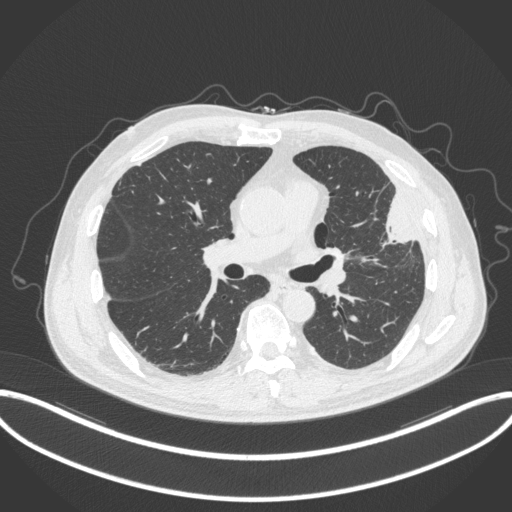
Chest CT, one axial slice. Slice 186 of 382 in the series (ordered by position). Reconstruction kernel B31f. Lung window (W 1500 / L -600 HU). 1 mm slice thickness. 512 × 512 image matrix, field of view 415 × 415 mm. Male patient, age 64 years. Case-level facts recorded for this patient, not image findings: clinical TNM (as recorded): T4 N1 M0; histopathological grade: G3.
Outlined on this slice (rectangle marked by the reading radiologist):
- lung tumour (recorded histology: adenocarcinoma): bounding box <369,186,419,248> (left, top, right, bottom; pixels)